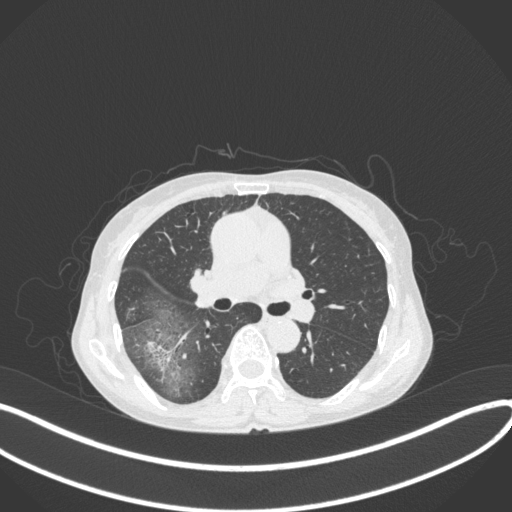
Chest CT, one axial slice; slice 232 of 379 in the series (ordered by position); reconstruction kernel B31f; 120 kVp; lung window (W 1500 / L -600 HU); 1 mm slice thickness; 512 × 512 image matrix, field of view 400 × 400 mm. Female patient, age 69 years. From the clinical record (not read from this slice): clinical TNM (as recorded): T1b N0 M0.
Structures marked on this image (rectangle marked by the reading radiologist):
- lung tumour (recorded histology: adenocarcinoma): box from (x=144, y=333) to (x=190, y=382) px